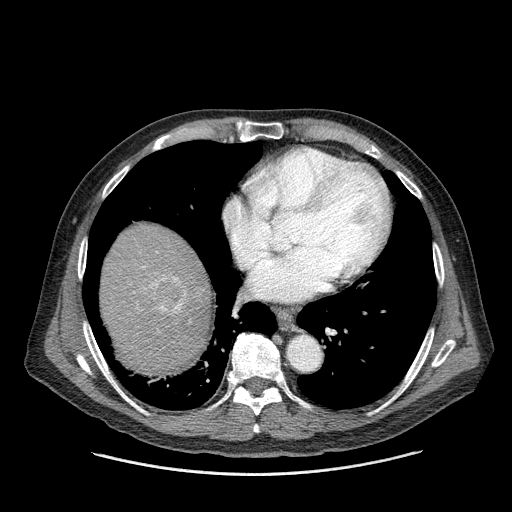
Contrast-enhanced abdominal CT (liver protocol), one axial slice. Position 148 of 180 along the scan axis. Reconstruction kernel STANDARD. 120 kVp. One of 2 acquisitions stored at this slice position. Soft-tissue window (W 400 / L 40 HU). 2.5 mm slice thickness. 512 × 512 image matrix, field of view 420 × 420 mm. Case-level facts recorded for this patient, not image findings: diagnosis: hepatocellular carcinoma (patient treated with transarterial chemoembolisation; whether this scan precedes or follows treatment is not stated here); TNM stage (as recorded): Stage-II; Child-Pugh class: A; tumour nodularity: multinodular; tumour size: 2.8 cm.
Annotated regions visible in this slice (semi-automatically segmented with operator editing):
- liver parenchyma outside the tumour (the mass and vessels are separate outlines, so this box may not span the whole liver): bounding box [x1, y1, x2, y2] px = [100, 224, 210, 374]
- mass: [152, 276, 189, 314]